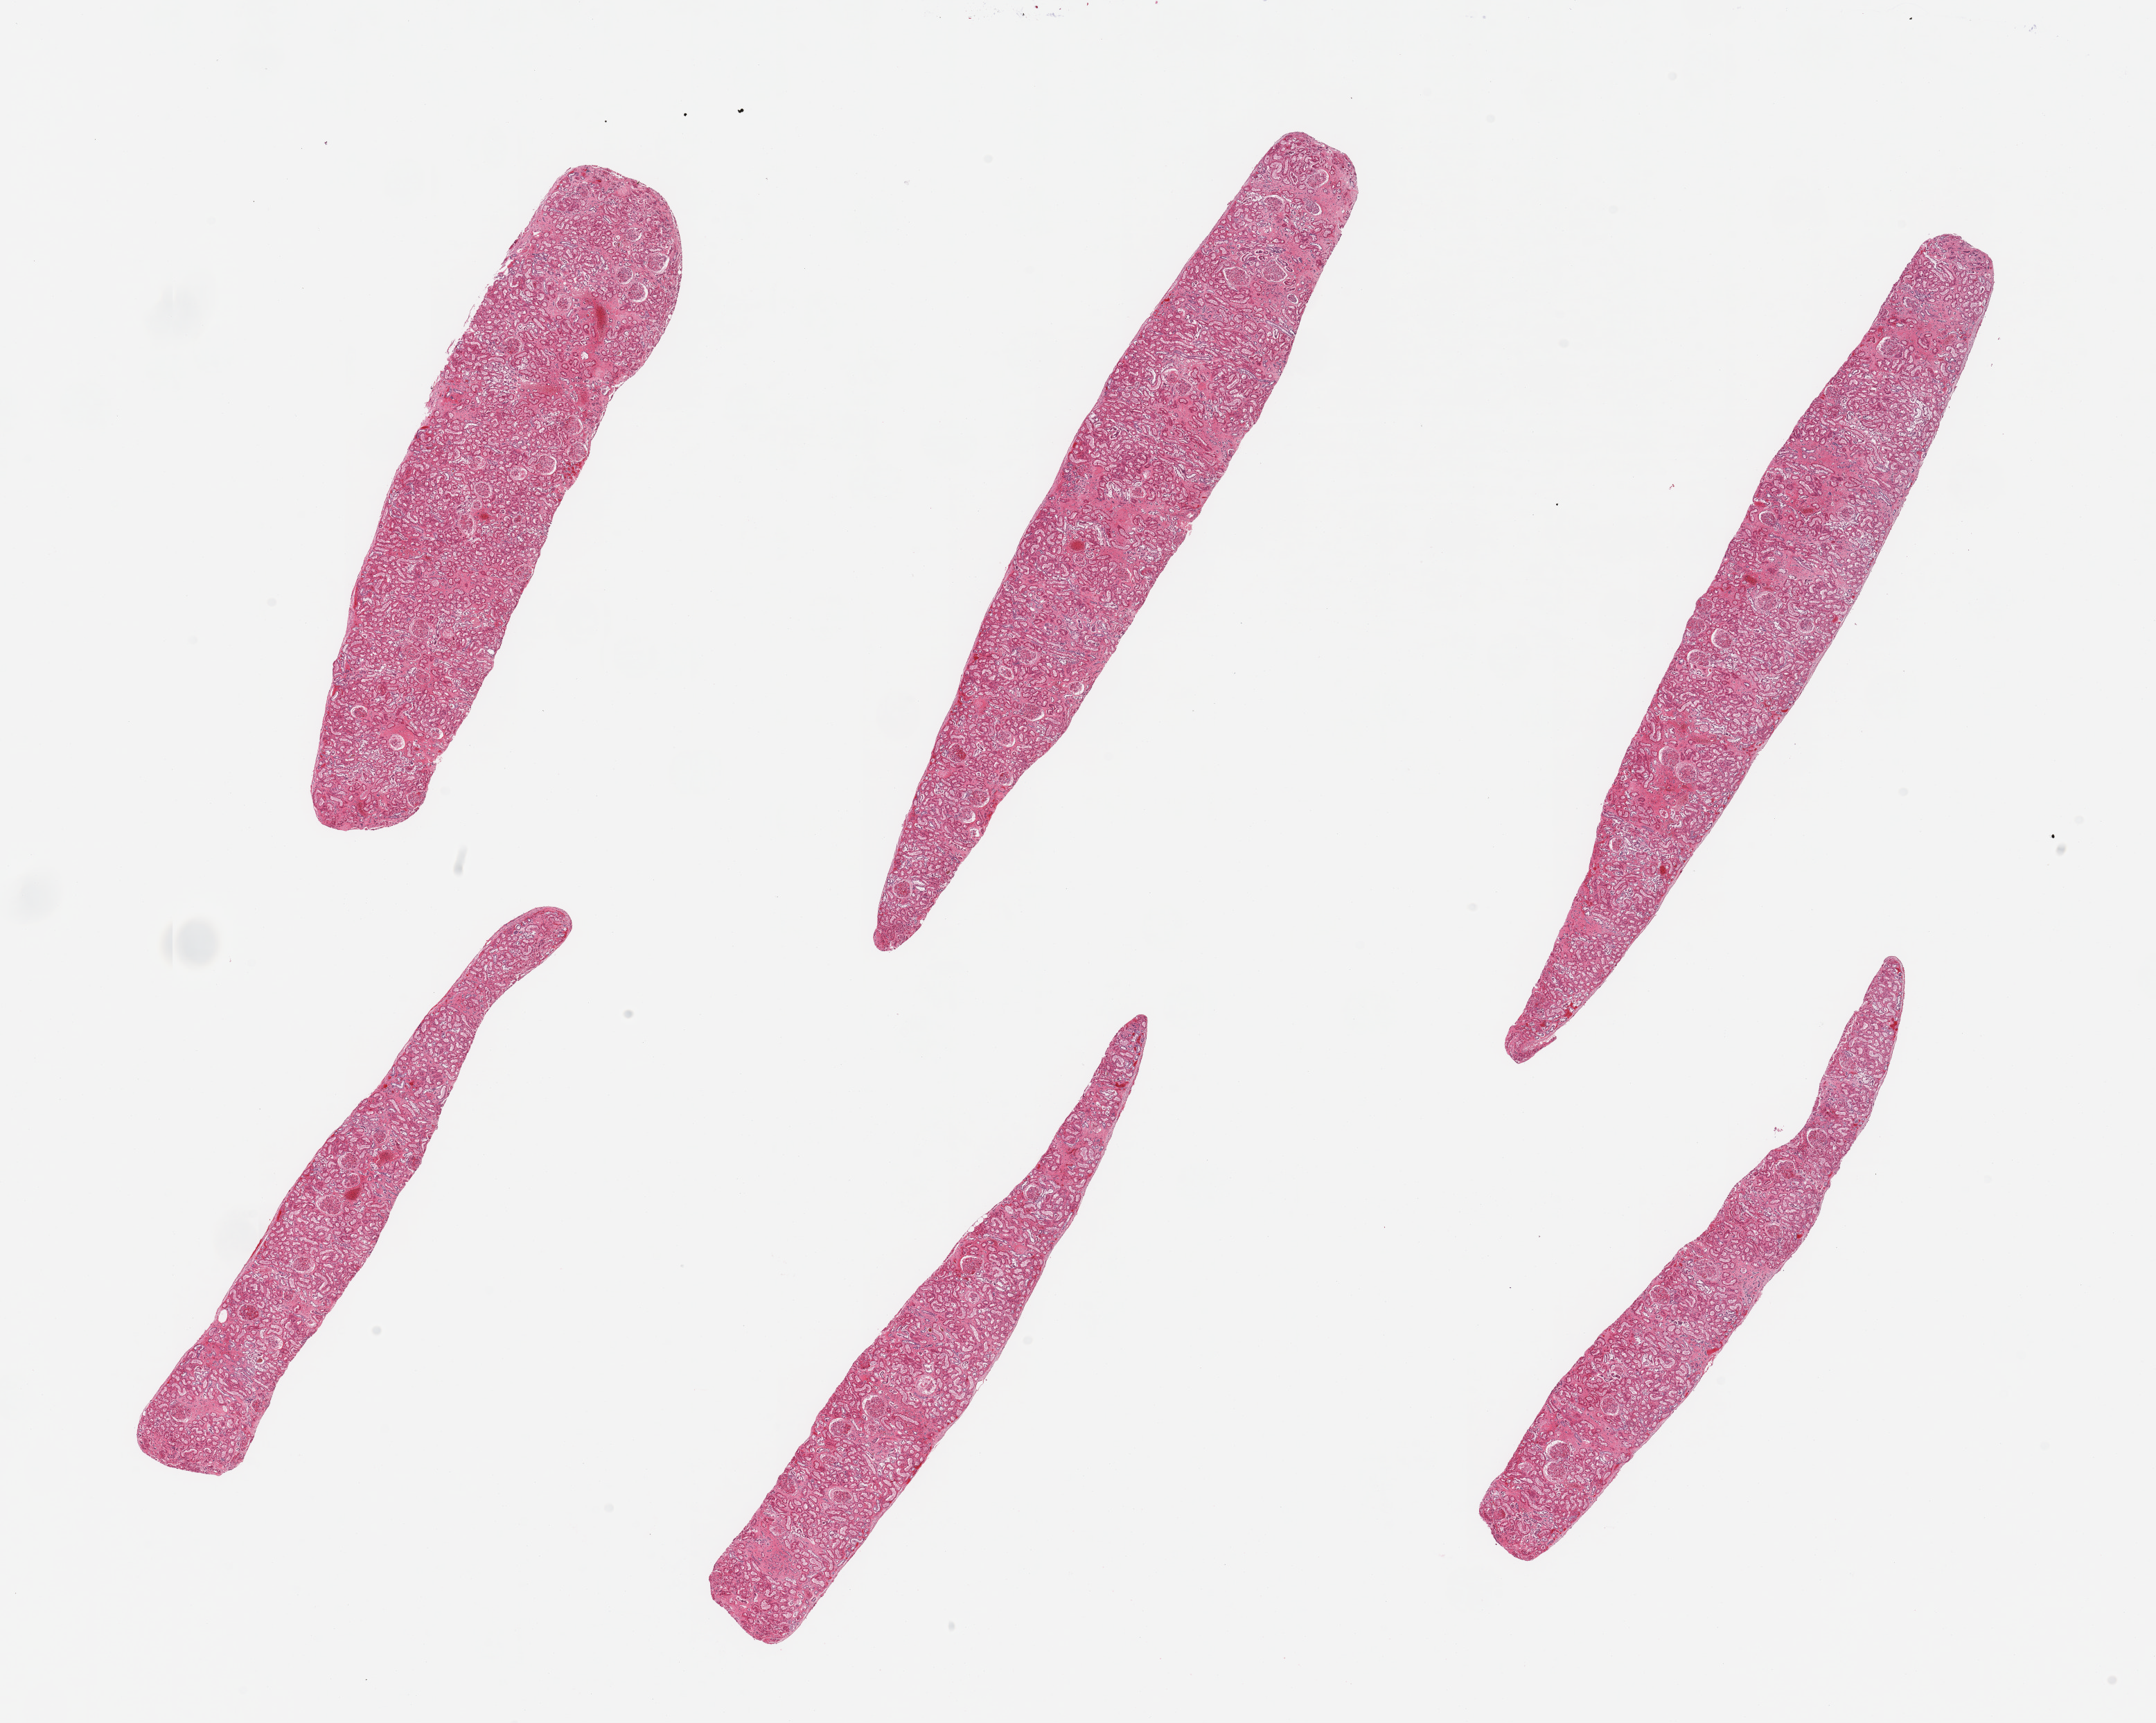
Whole-slide image, hematoxylin and eosin (H&E) stain, low-resolution overview of the scanned area, about 24.6 x 19.7 mm. PAXgene-fixed, paraffin-embedded tissue. Section of renal cortex (target tissue). Tissue donor sample. Donor sex: male.
Reviewer comment on this tissue sample: 6 pieces, glomeruli present, advanced tubular autolysis.